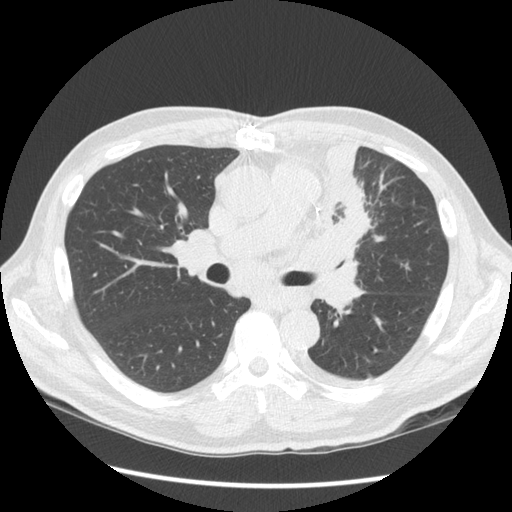
Low-dose screening chest CT, one axial slice; position 84 of 136 along the scan axis; reconstruction kernel STANDARD; lung window (W 1500 / L -600 HU); 2.5 mm slice thickness; 512 × 512 image matrix, field of view 360 × 360 mm.
Annotated regions visible in this slice (manually delineated by an expert):
- lesion 1 (tumor, upper lobe of left lung): bounding box [x1, y1, x2, y2] px = [307, 142, 371, 281]